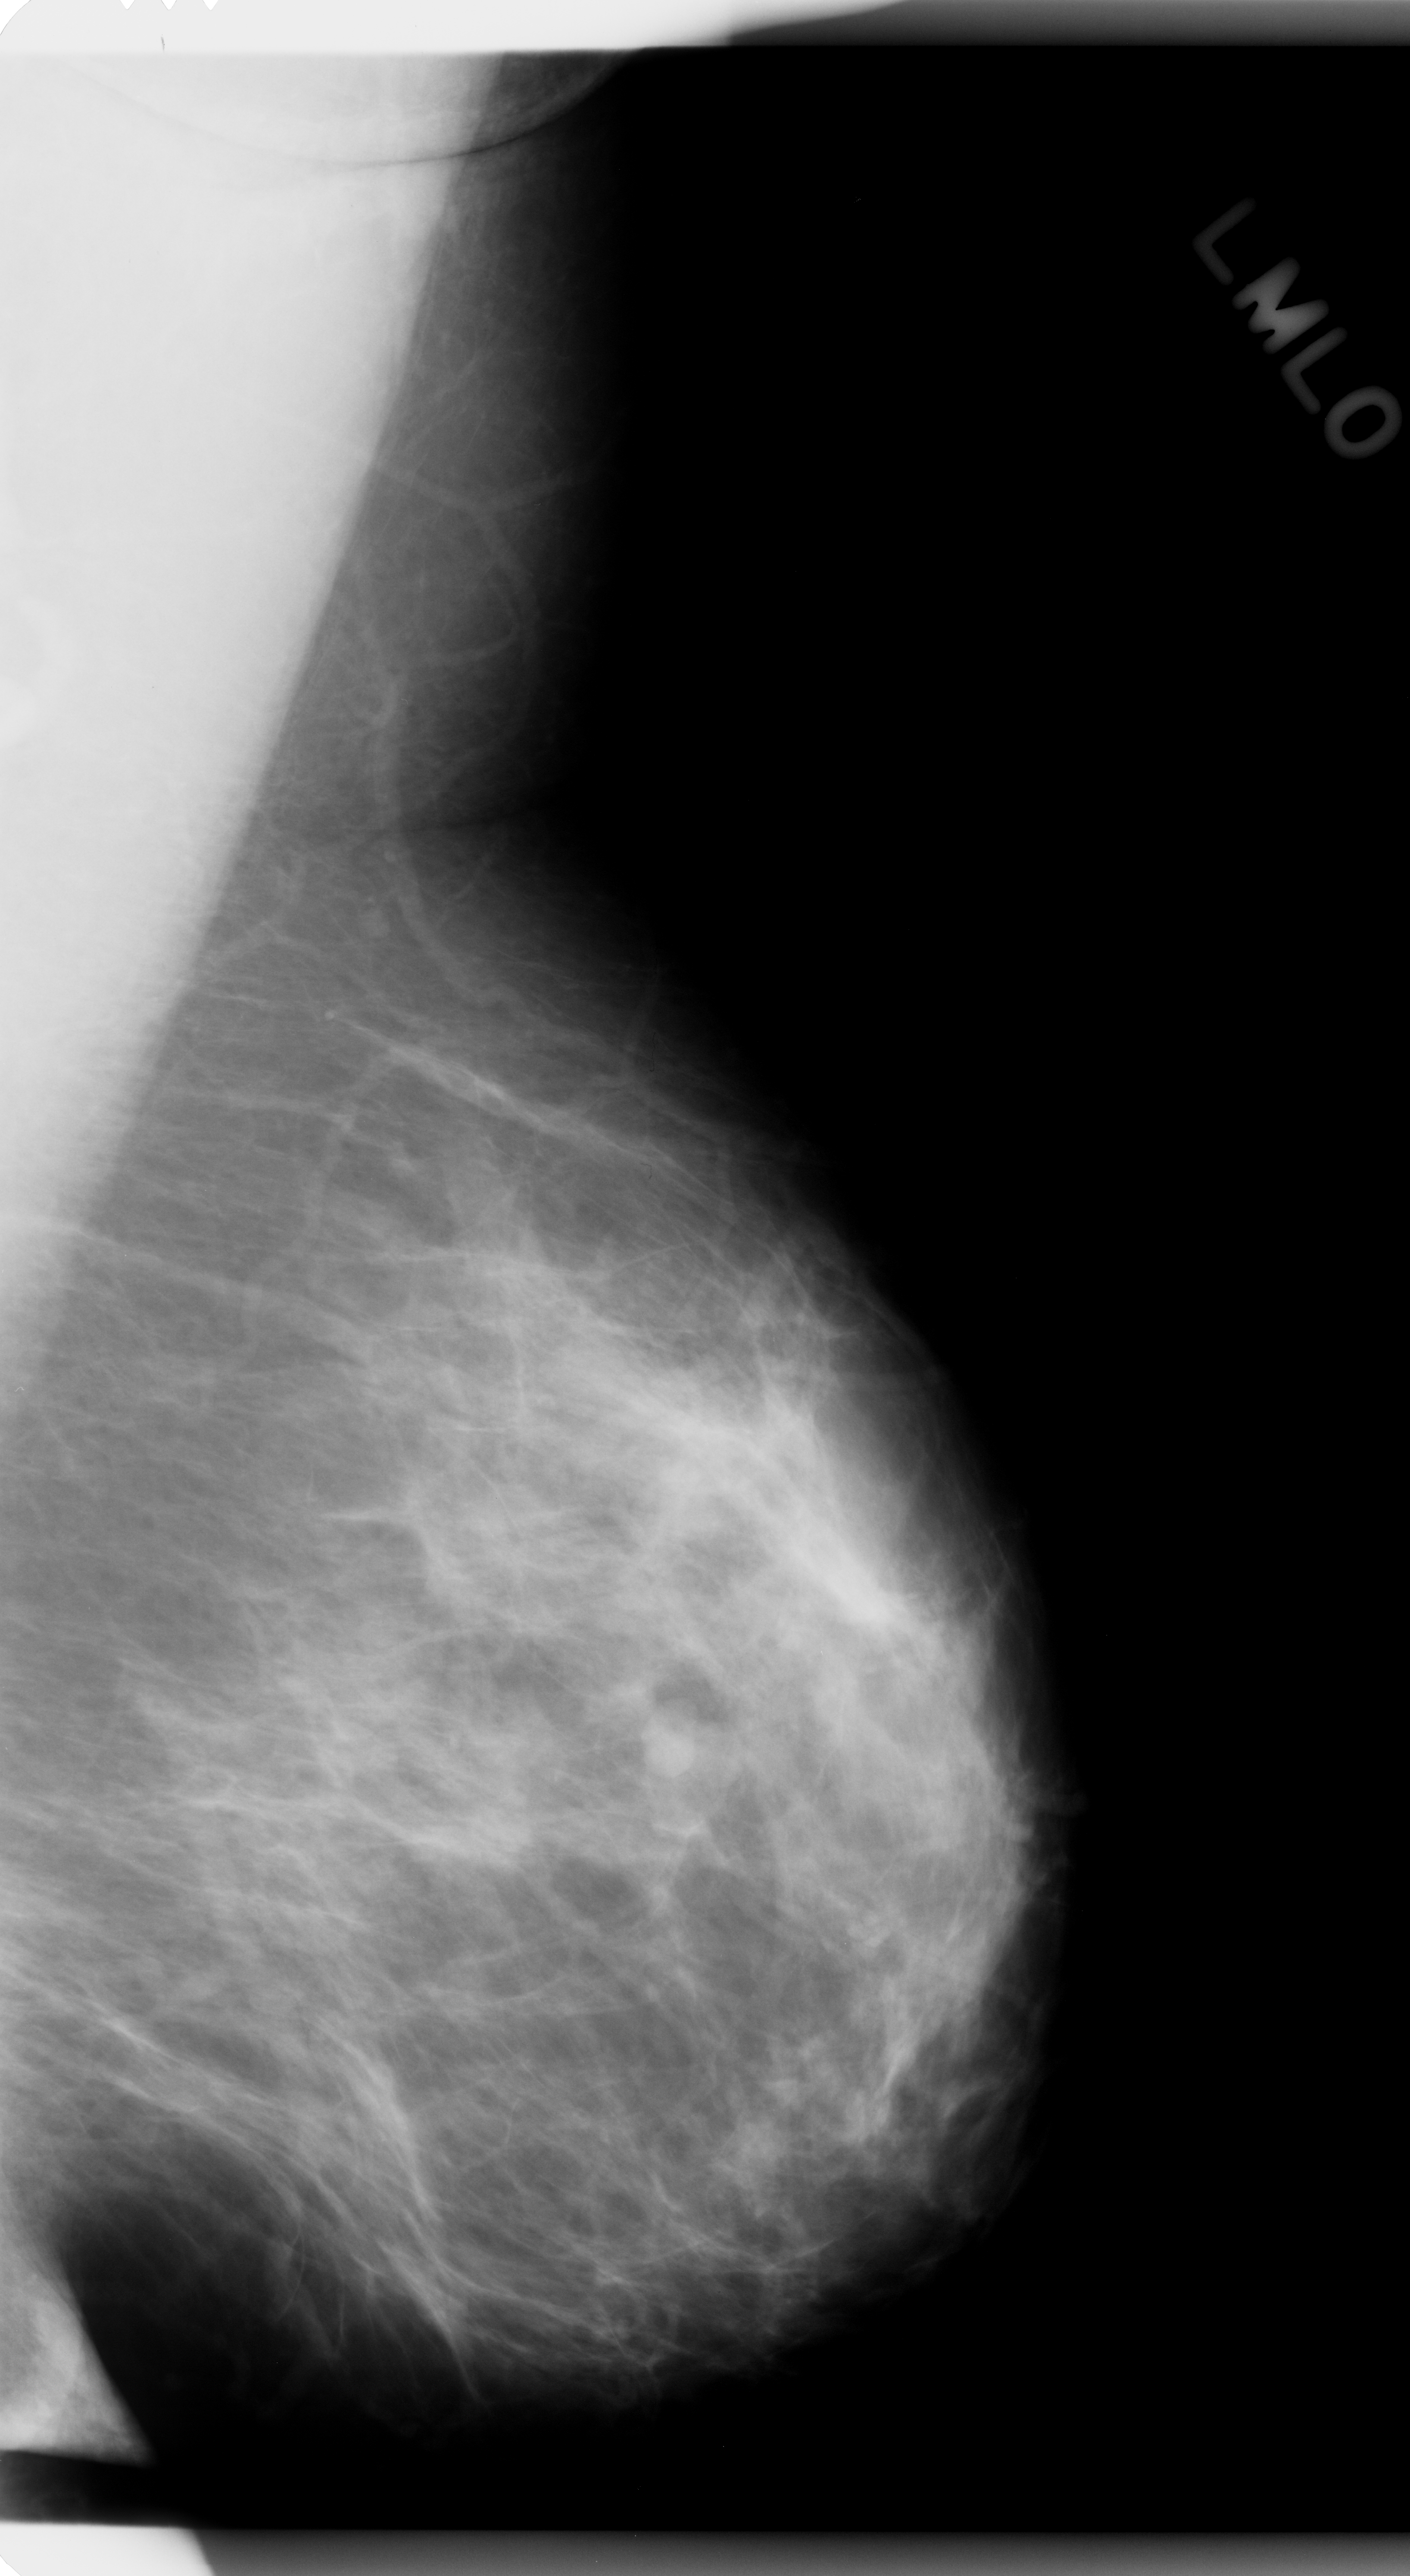
Digitized screen-film mammogram; left breast; MLO view; BI-RADS breast density category 2 (scale 1–4); 1410 × 2576 image matrix.
Marked abnormalities (boxes around the expert regions of interest):
- mass, shape lobulated, margins circumscribed; BI-RADS assessment category 3; subtlety rating 4 on a 1 (subtle) to 5 (obvious) scale; pathology result (as recorded, not read from the image): benign: bounding box (x1, y1, x2, y2) in pixels: (641, 1722, 699, 1782)